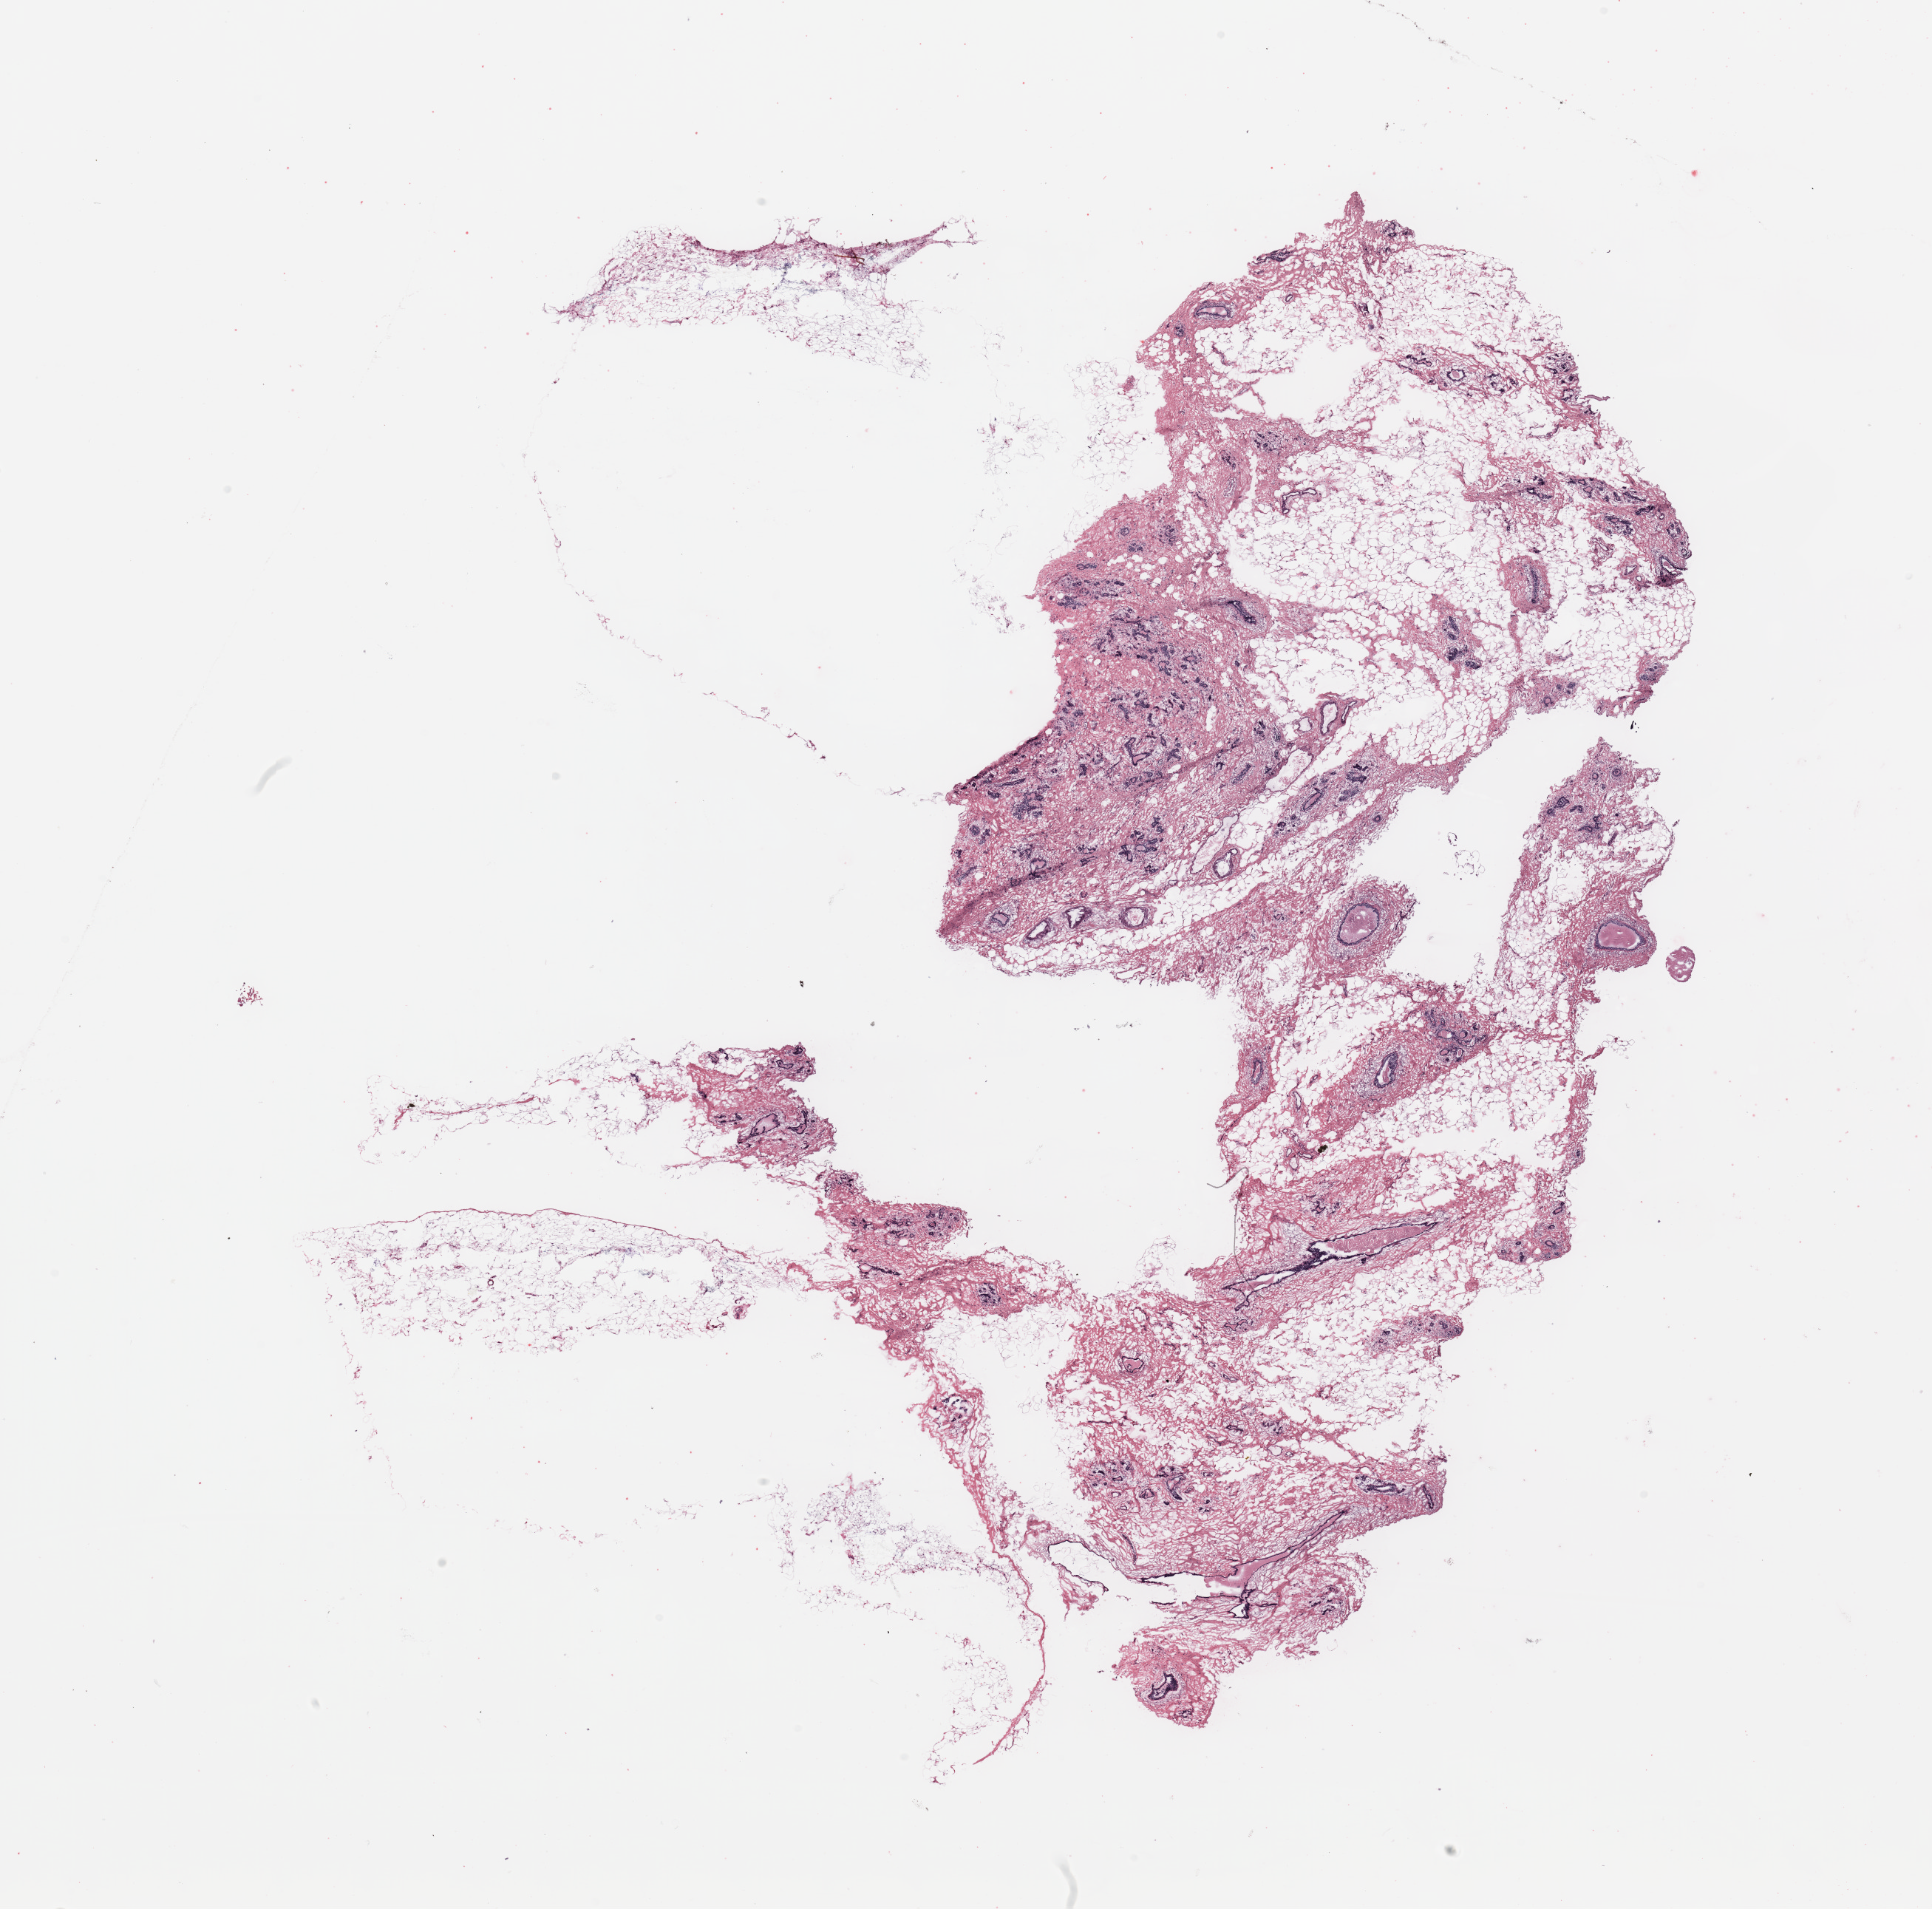
H&E whole-slide image, whole scanned area (about 20.7 x 20.4 mm, acquisition: 20x scan) shown as a low-resolution overview; breast, tissue type not recorded.
Patient diagnosis (cohort enrolment): breast cancer (breast).